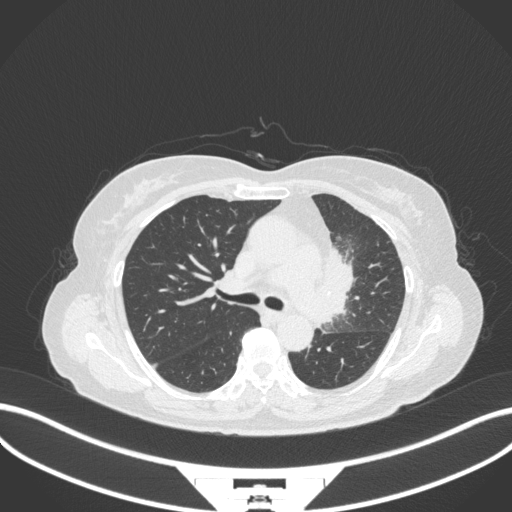
Chest CT, one axial slice; slice 212 of 382 in the series (ordered by position); reconstruction kernel B31f; lung window (W 1500 / L -600 HU); 1 mm slice thickness; 512 × 512 image matrix, field of view 400 × 400 mm. Patient: female, 64 years. From the clinical record (not read from this slice): clinical TNM (as recorded): T2a N2 M0.
Annotated regions visible in this slice (bounding box drawn by a radiologist):
- lung tumour (recorded histology: adenocarcinoma): bounding box <319,242,353,331> (left, top, right, bottom; pixels)